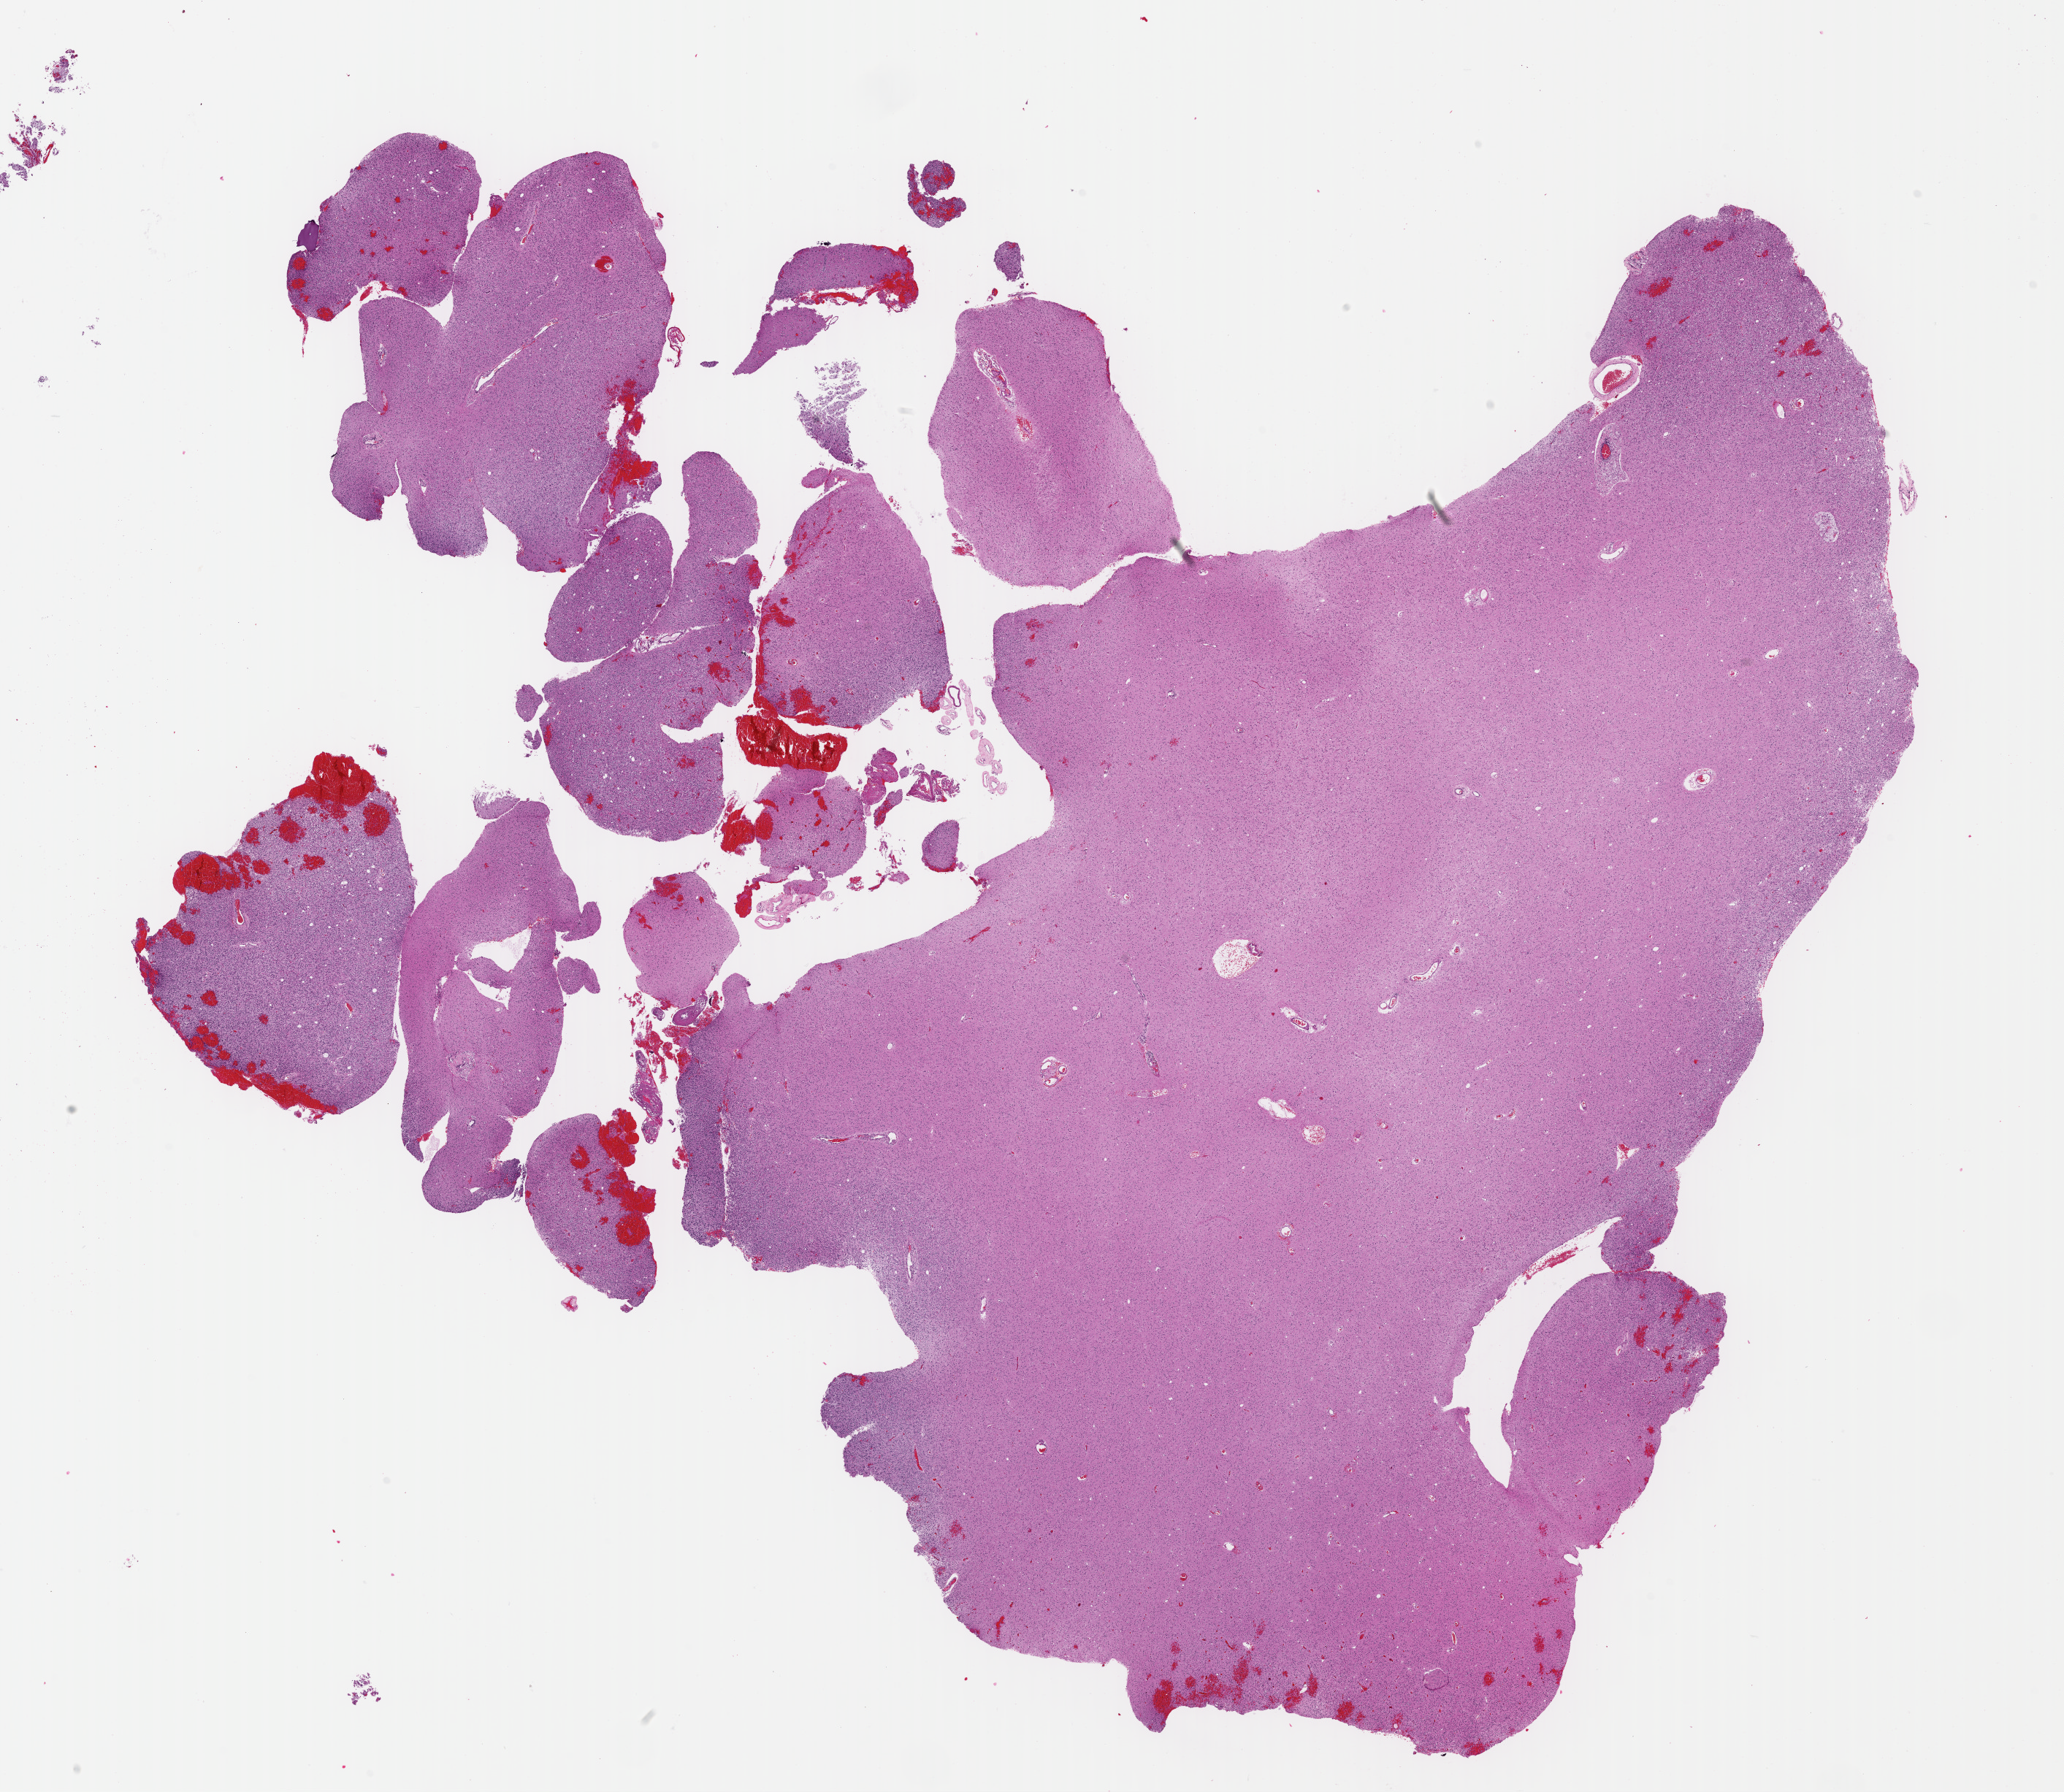
Digitized H&E-stained tissue section (whole slide), low-resolution overview of the scanned area, about 22.2 x 19.3 mm. Formalin-fixed paraffin-embedded (FFPE) diagnostic section. Sample: primary tumour, brain. Female patient; age at initial diagnosis 34 years. Histologic grade: G2 (moderately differentiated).
* pathologic diagnosis: Mixed glioma (cerebrum)